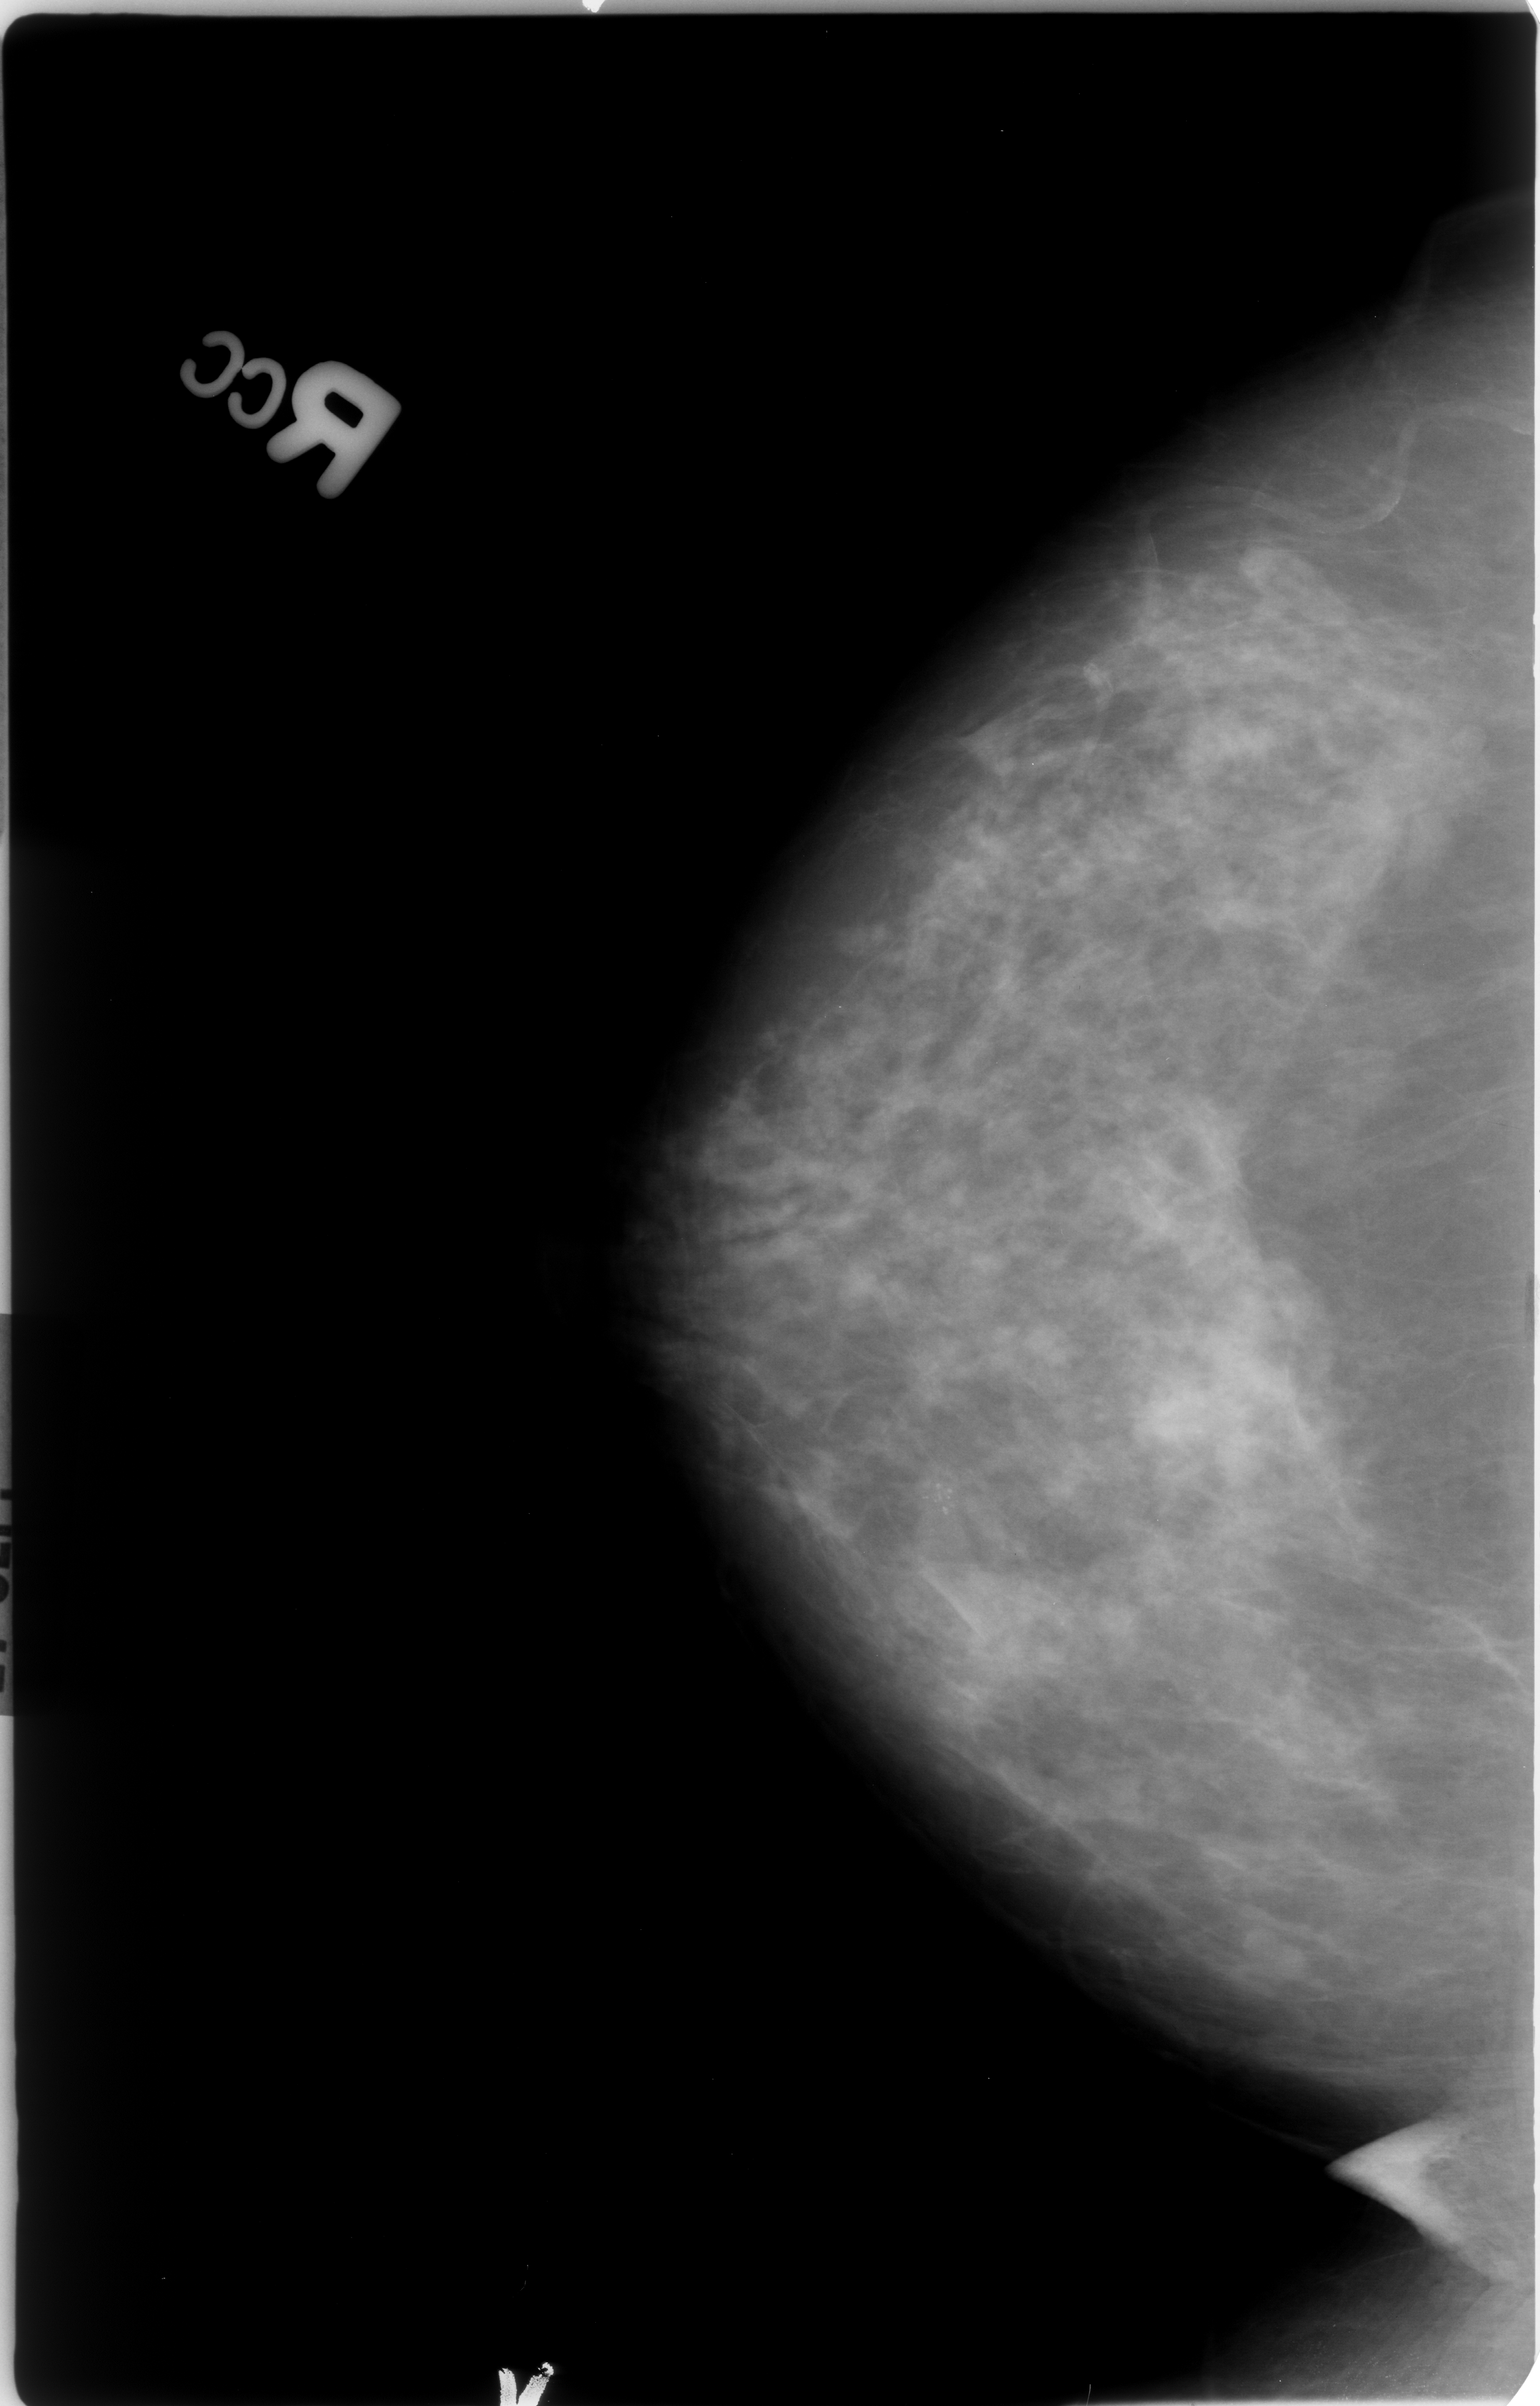
Digitized screen-film mammogram; right breast; craniocaudal (CC) view; BI-RADS breast density category 3 (scale 1–4).
- Finding: calcifications, morphology pleomorphic, distribution clustered; BI-RADS assessment category 4; subtlety rating 3 on a 1 (subtle) to 5 (obvious) scale; pathology result (as recorded, not read from the image): malignant.